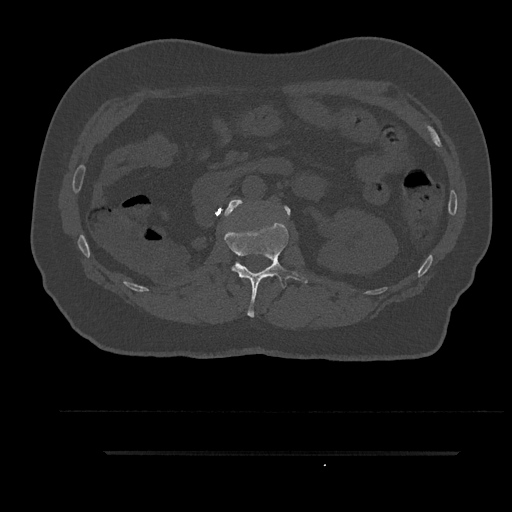
CT including the spine, one axial slice. Slice 163 of 797 in the series (ordered by position). Reconstruction kernel Br40s/3. Bone window (W 1800 / L 400 HU). 0.5 mm slice thickness. 512 × 512 image matrix, field of view 432 × 432 mm. Patient: male, 63 years. Case-level facts recorded for this patient, not image findings: primary cancer: renal; vertebrae with lytic lesions (as recorded): T8.
Annotated regions visible in this slice (semi-automatic segmentation, software-assisted and operator-edited):
- L1 vertebra: bounding box (x1, y1, x2, y2) in pixels: (225, 222, 308, 318)
- L2 vertebra: (224, 199, 291, 216)